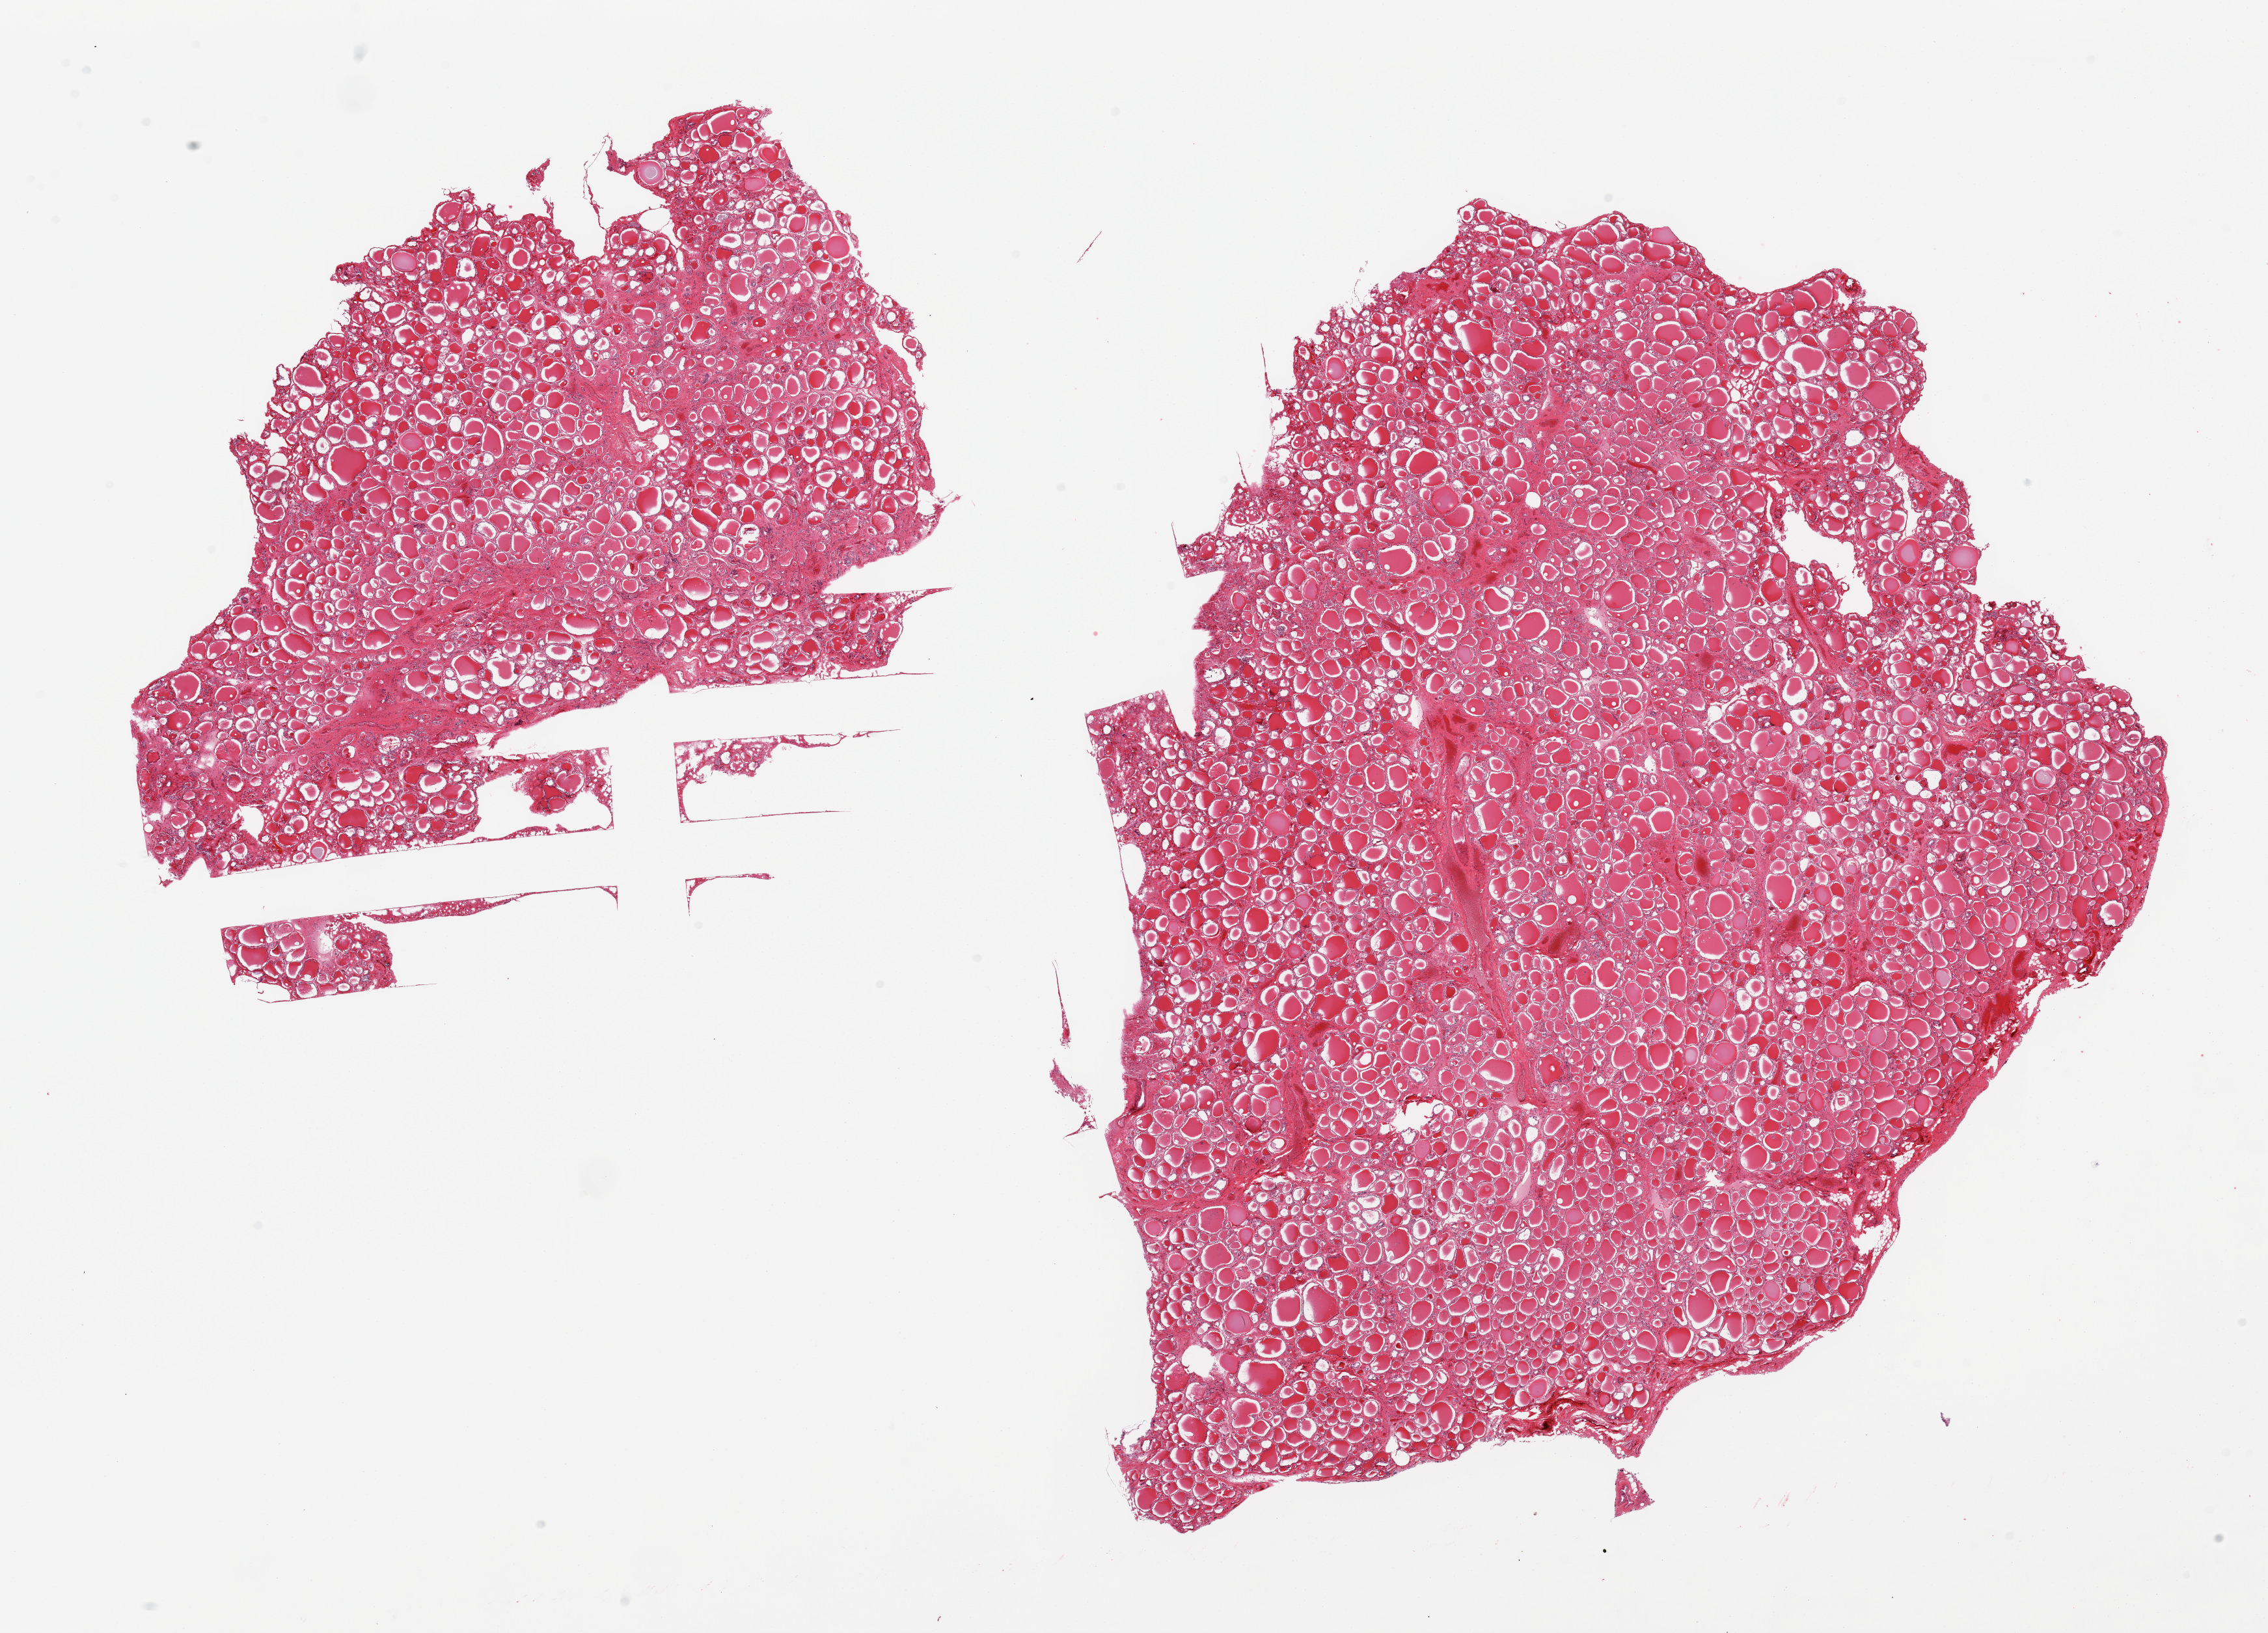
Digitized haematoxylin and eosin-stained section, a low-resolution overview of the entire scanned area, about 27.6 x 19.9 mm (from a 20x scan); PAXgene-fixed, paraffin-embedded tissue; section of thyroid (target tissue); donor tissue sample. Donor sex: male.
• review note (as recorded): 2 pieces